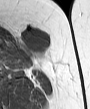
MRI of an extremity soft-tissue mass, one axial slice; position 24 of 45 along the scan axis; MR volume resampled by the dataset authors to the PET/CT grid (not the native acquisition matrix); 3.27 mm slice thickness; 90 × 109 image matrix, field of view 88 × 106 mm. Female patient. From the clinical record (not read from this slice): histological type: leiomyosarcoma; grade: intermediate; site of the primary tumour: parascapusular.
Outlined on this slice (expert contour drawn on MRI and transferred to this co-registered scan by the dataset authors):
- gross tumour volume including surrounding oedema: box from (x=17, y=27) to (x=50, y=65) px
- gross tumour volume (mass): (x=21, y=27)–(x=50, y=56)